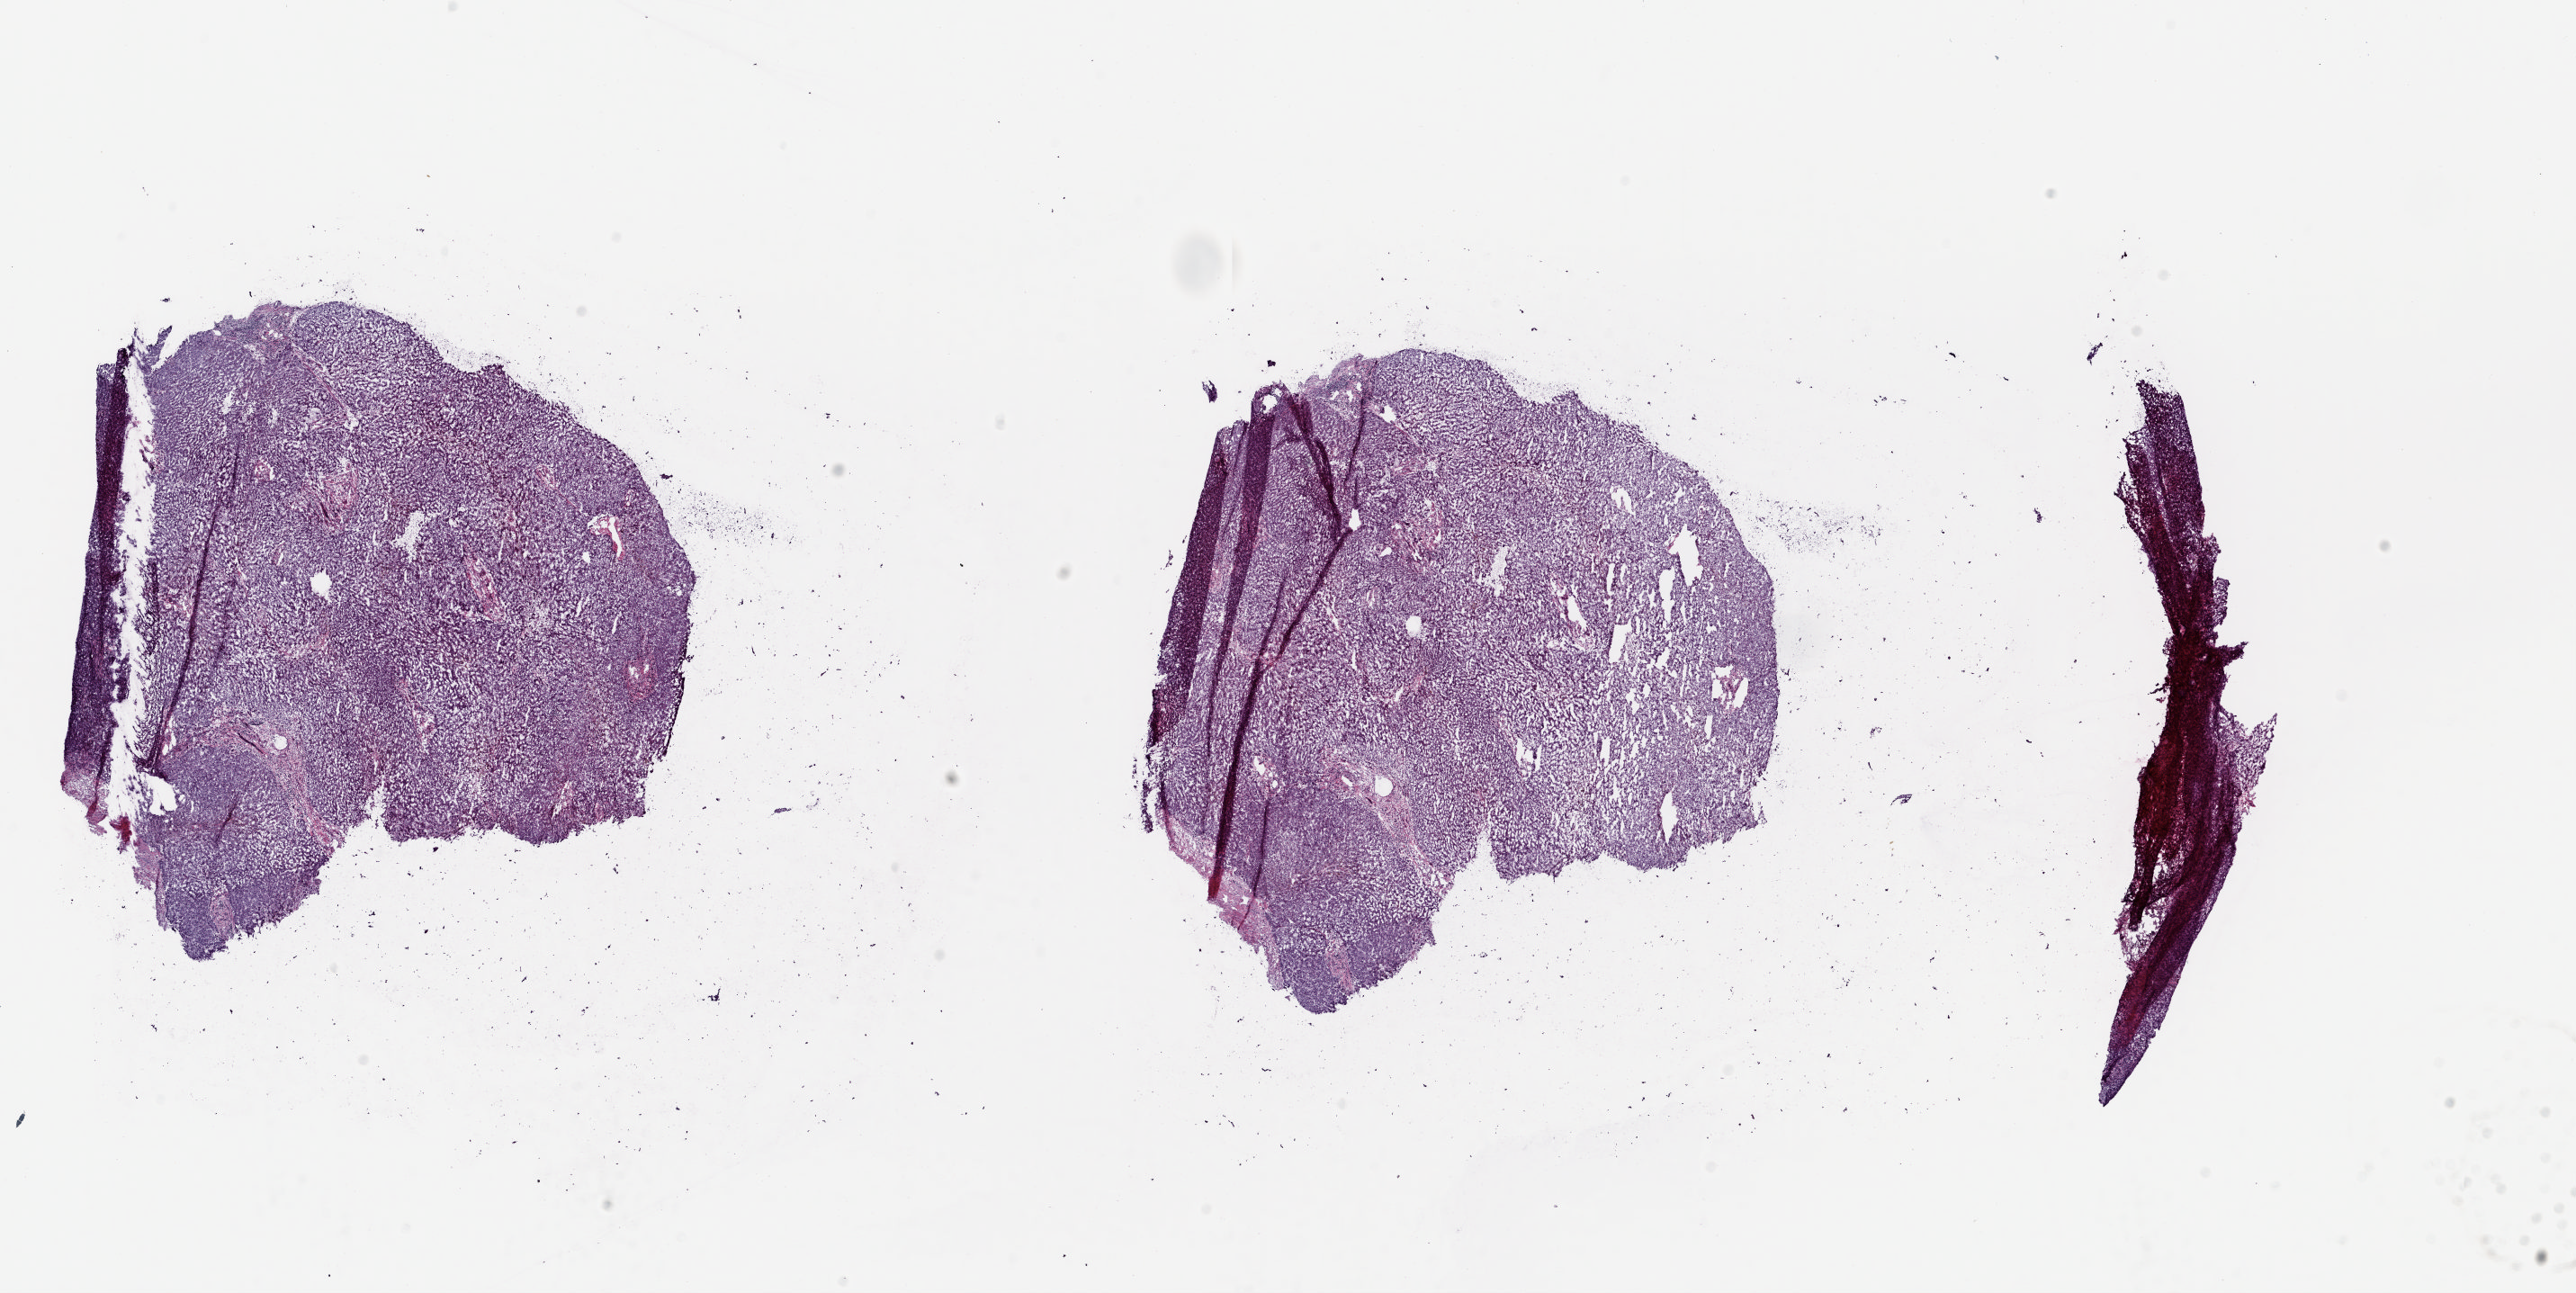
Whole-slide histology image, Hematoxylin and eosin (H&E) stained — shown as a low-resolution overview of the whole scanned area (about 22.7 x 11.4 mm, from a 20x scan); frozen section from the top of the tissue portion; liver, solid tissue normal (non-tumour tissue) sample. Patient: male, age at initial diagnosis 80 years. Slide review estimates, as recorded: tumour cells 0%, tumour nuclei 0%.
This section: solid tissue normal (non-tumour) sample from the same patient. Patient diagnosis: Hepatocellular carcinoma, NOS.